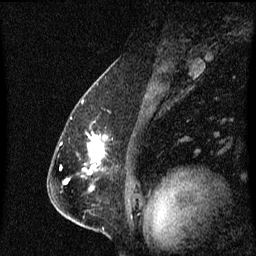
Breast MRI (dynamic contrast-enhanced), one sagittal slice. Slice 42 of 60 in the series (ordered by position). Dynamic contrast-enhanced series, image 2 of 3 at this slice position (ordered by acquisition). 1.5 T. TE 4.2 ms, TR 8.4 ms. 2 mm slice thickness. 256 × 256 image matrix. Patient: female, 57 years. From the clinical record (not read from this slice): setting: breast cancer imaged before/during neoadjuvant chemotherapy; receptor status: HR-positive, HER2-negative.
Outlined on this slice (semi-automatic segmentation, software-assisted and operator-edited):
- analysis volume of interest (the breast-tissue region the enhancement analysis was run in; not a lesion): bounding box [x1, y1, x2, y2] px = [82, 122, 104, 177]
- tumour enhancement mask (voxels above the 70 % enhancement threshold inside the analysis volume of interest): [88, 134, 104, 169]